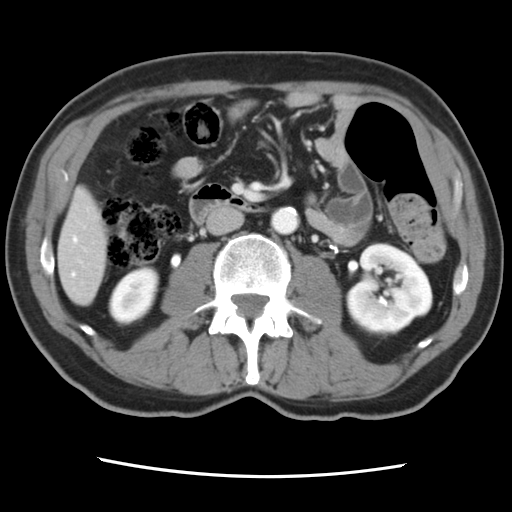
Contrast-enhanced abdominal CT, one axial slice. Position 22 of 83 along the scan axis. Intravenous contrast given. Soft-tissue window (W 400 / L 40 HU). 5 mm slice thickness. 512 × 512 image matrix, field of view 321 × 321 mm. Male patient, age 69 years. Case-level facts recorded for this patient, not image findings: diagnosis: colorectal cancer liver metastases, imaged before liver resection; multiple liver metastases: yes; largest metastasis: 3.5 cm; chemotherapy before resection: yes.
Annotated regions visible in this slice (outlined manually by an expert reader):
- hepatic veins: bounding box <72,237,77,276> (left, top, right, bottom; pixels)
- liver: <59,191,108,304>
- planned liver remnant (the part of the liver to remain after resection): <59,191,108,304>